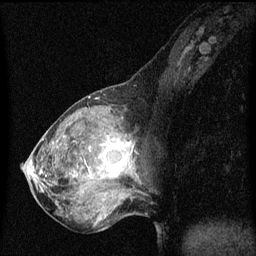
Breast MRI (dynamic contrast-enhanced), one sagittal slice. Slice 24 of 60 in the series (ordered by position). Dynamic contrast-enhanced series, image 2 of 3 at this slice position (ordered by acquisition). 1.5 T. TE 4.2 ms, TR 8 ms. 256 × 256 image matrix. Female patient, age 50 years.
Structures marked on this image (semi-automatically segmented with operator editing):
- analysis volume of interest (the breast-tissue region the enhancement analysis was run in; not a lesion): box from (x=91, y=126) to (x=140, y=189) px
- tumour enhancement mask (voxels above the 70 % enhancement threshold inside the analysis volume of interest): (x=101, y=138)–(x=131, y=177)